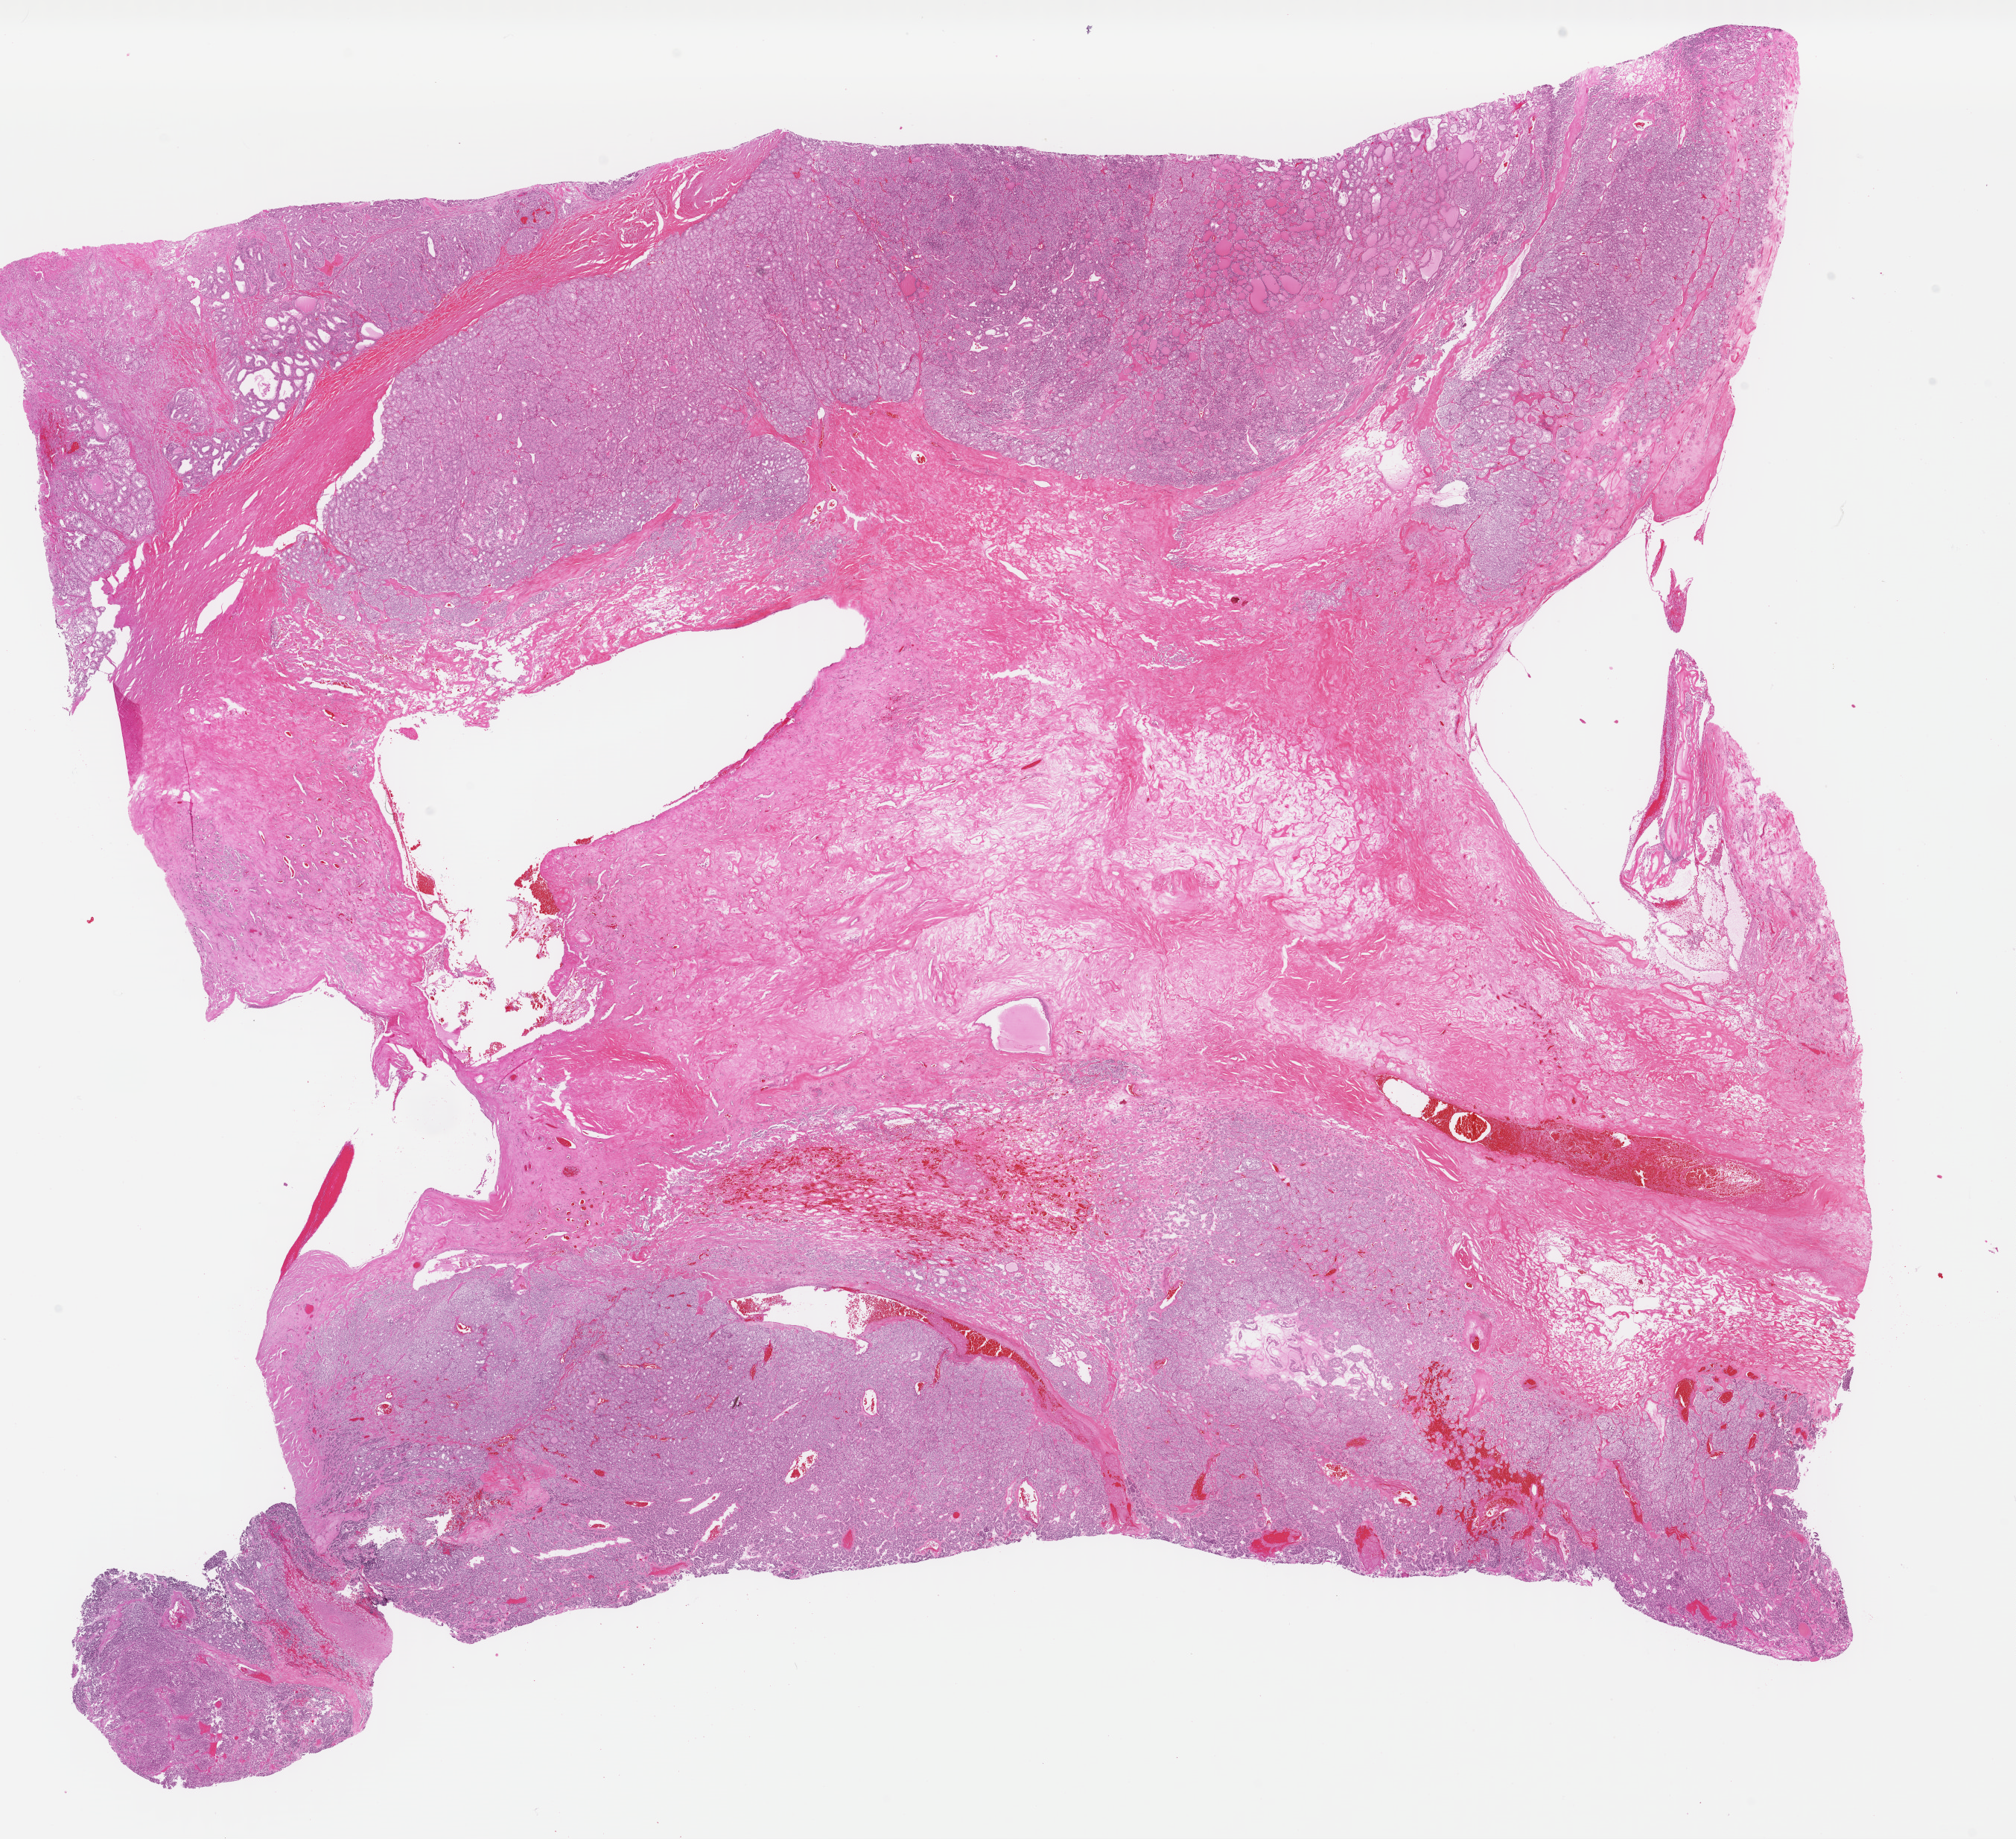
Digitized Hematoxylin and eosin (H&E) stained tissue section (whole slide), shown as a low-resolution overview of the whole scanned area (about 21.3 x 19.4 mm, acquisition: 40x scan). Formalin-fixed paraffin-embedded (FFPE) diagnostic section. Primary tumour sample from the thyroid. Male, age 63 years at initial diagnosis.
TNM: T3 N0 MX. AJCC pathologic stage: III (7th edition). Histologic diagnosis: Papillary adenocarcinoma, NOS (thyroid gland). Lymph nodes positive (case pathology): 0 of 1 examined.